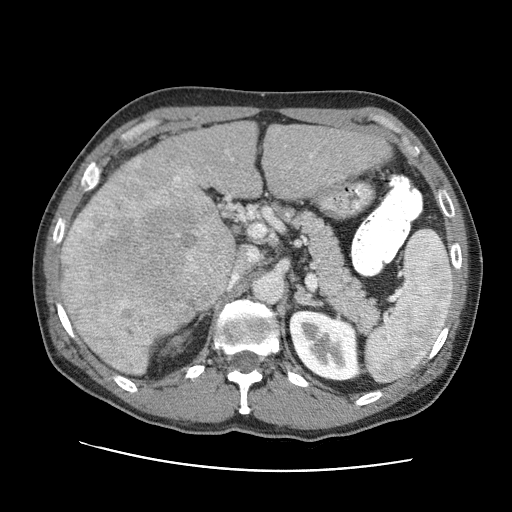
Contrast-enhanced abdominal CT (liver protocol), one axial slice; slice 46 of 95 in the series (ordered by position); one of 2 acquisitions stored at this slice position; soft-tissue window (W 400 / L 40 HU); 512 × 512 image matrix. From the clinical record (not read from this slice): diagnosis: hepatocellular carcinoma (patient treated with transarterial chemoembolisation; whether this scan precedes or follows treatment is not stated here); TNM stage (as recorded): Stage-IVA; Child-Pugh class: A; tumour nodularity: multinodular.
Annotated regions visible in this slice (semi-automatic segmentation, software-assisted and operator-edited):
- liver parenchyma outside the tumour (the mass and vessels are separate outlines, so this box may not span the whole liver): bounding box [x1, y1, x2, y2] px = [80, 122, 390, 270]
- mass: [63, 157, 236, 373]
- liver vessels: [179, 150, 313, 198]